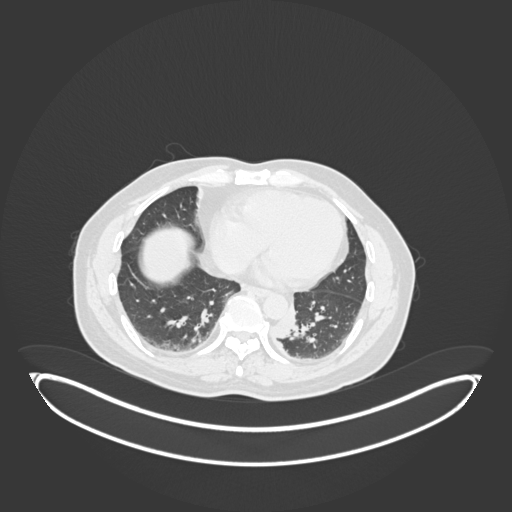
Chest CT, one axial slice; position 55 of 258 along the scan axis; 120 kVp; lung window (W 1500 / L -600 HU); 1 mm slice thickness; 512 × 512 image matrix, field of view 500 × 500 mm. Male patient, age 54 years. Case-level facts recorded for this patient, not image findings: clinical TNM (as recorded): T3 N0 M0.
Outlined on this slice (bounding box drawn by a radiologist):
- lung tumour (recorded histology: squamous cell carcinoma): bounding box <276,309,302,342> (left, top, right, bottom; pixels)